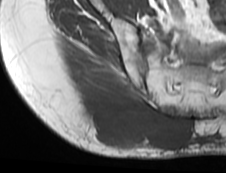
MRI of an extremity soft-tissue mass, one axial slice. Position 48 of 73 along the scan axis. MR volume resampled by the dataset authors to the PET/CT grid (not the native acquisition matrix). 3.27 mm slice thickness. 226 × 173 image matrix, field of view 221 × 169 mm. Female patient. Case-level facts recorded for this patient, not image findings: histological type: spindle cell suggestive of myxofibrosarcoma; grade: intermediate; site of the primary tumour: right buttock.
Structures marked on this image (expert contour drawn on MRI and transferred to this co-registered scan by the dataset authors):
- gross tumour volume (mass): bounding box <75,88,190,150> (left, top, right, bottom; pixels)